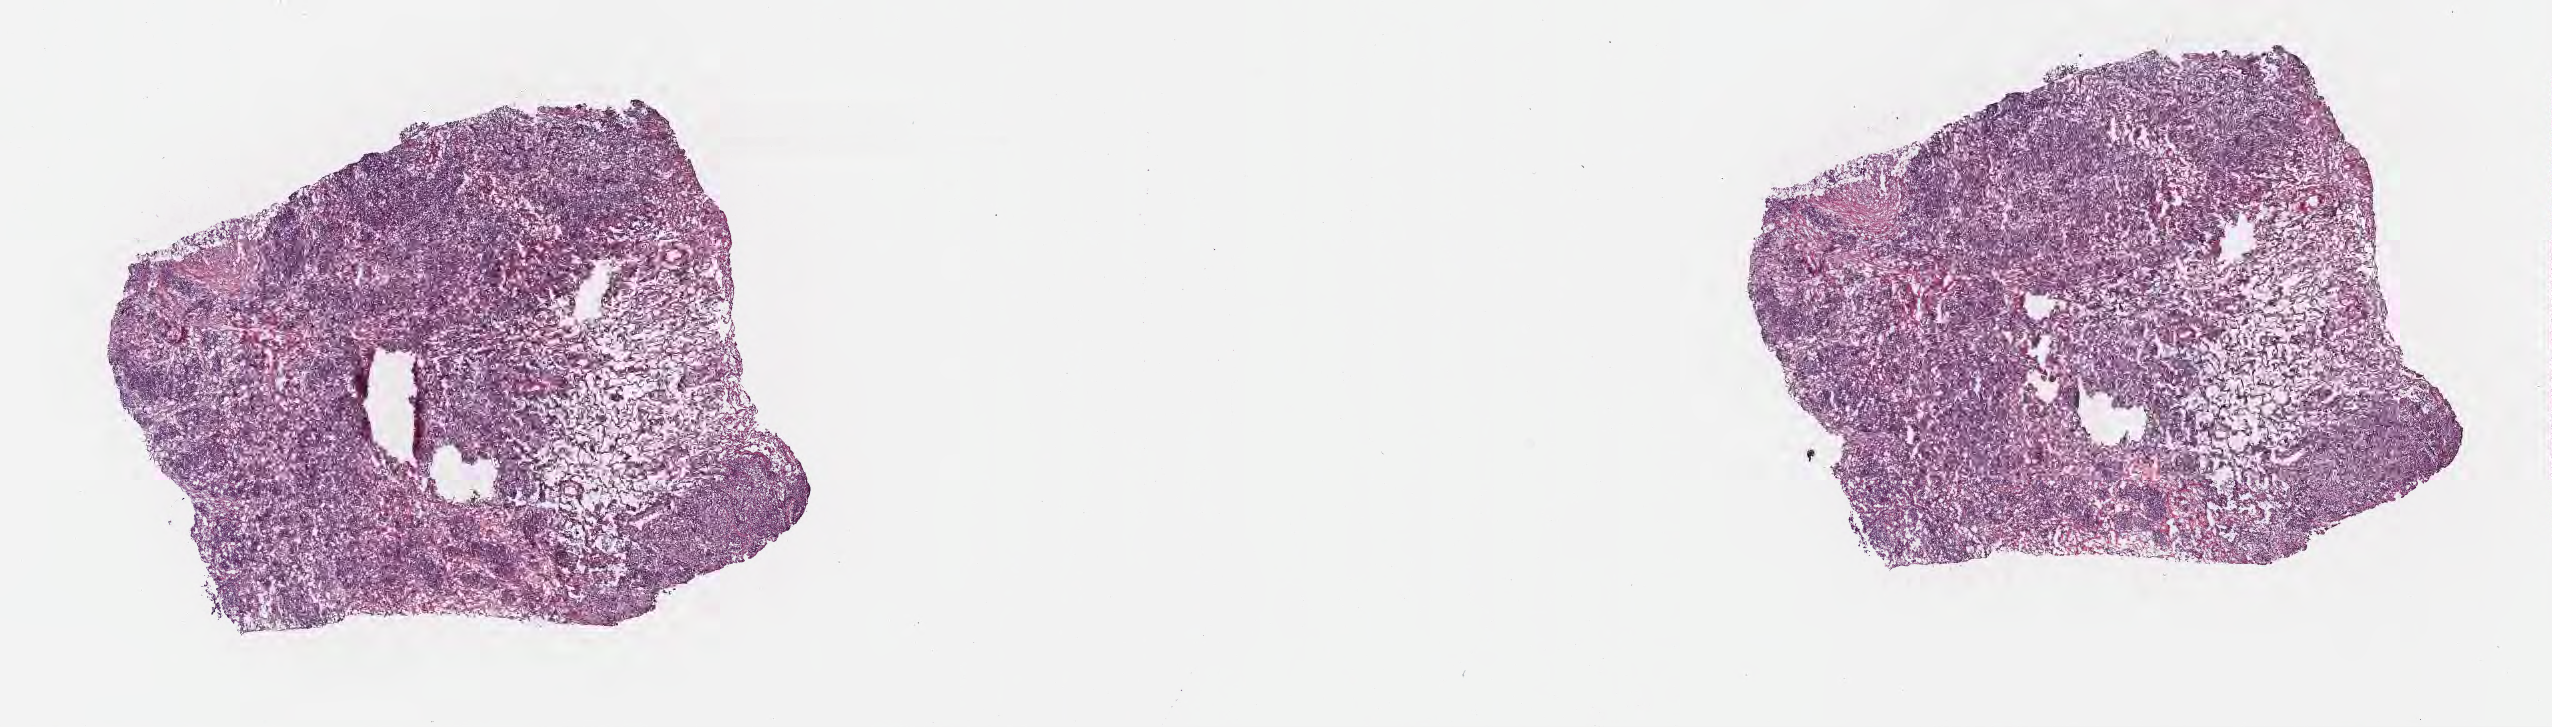
Digitized H&E-stained section — whole scanned area (about 20.6 x 5.9 mm) shown as a low-resolution overview. Frozen section (tissue freezing medium). Specimen: primary tumor. Site: lower lobe of right lung. Male patient, age 74 years. Composition of this section per pathologist review: tumor cells 51%, tumor nuclei 70%, stromal cells 25%, necrosis 1%, normal cells 23%. Inflammatory infiltration, as recorded: lymphocyte infiltration 17%, monocyte infiltration 2%, neutrophil infiltration 2%.
Section: top of the tissue portion. Histologic diagnosis: Acinar cell carcinoma. AJCC pathologic stage: Stage IB.